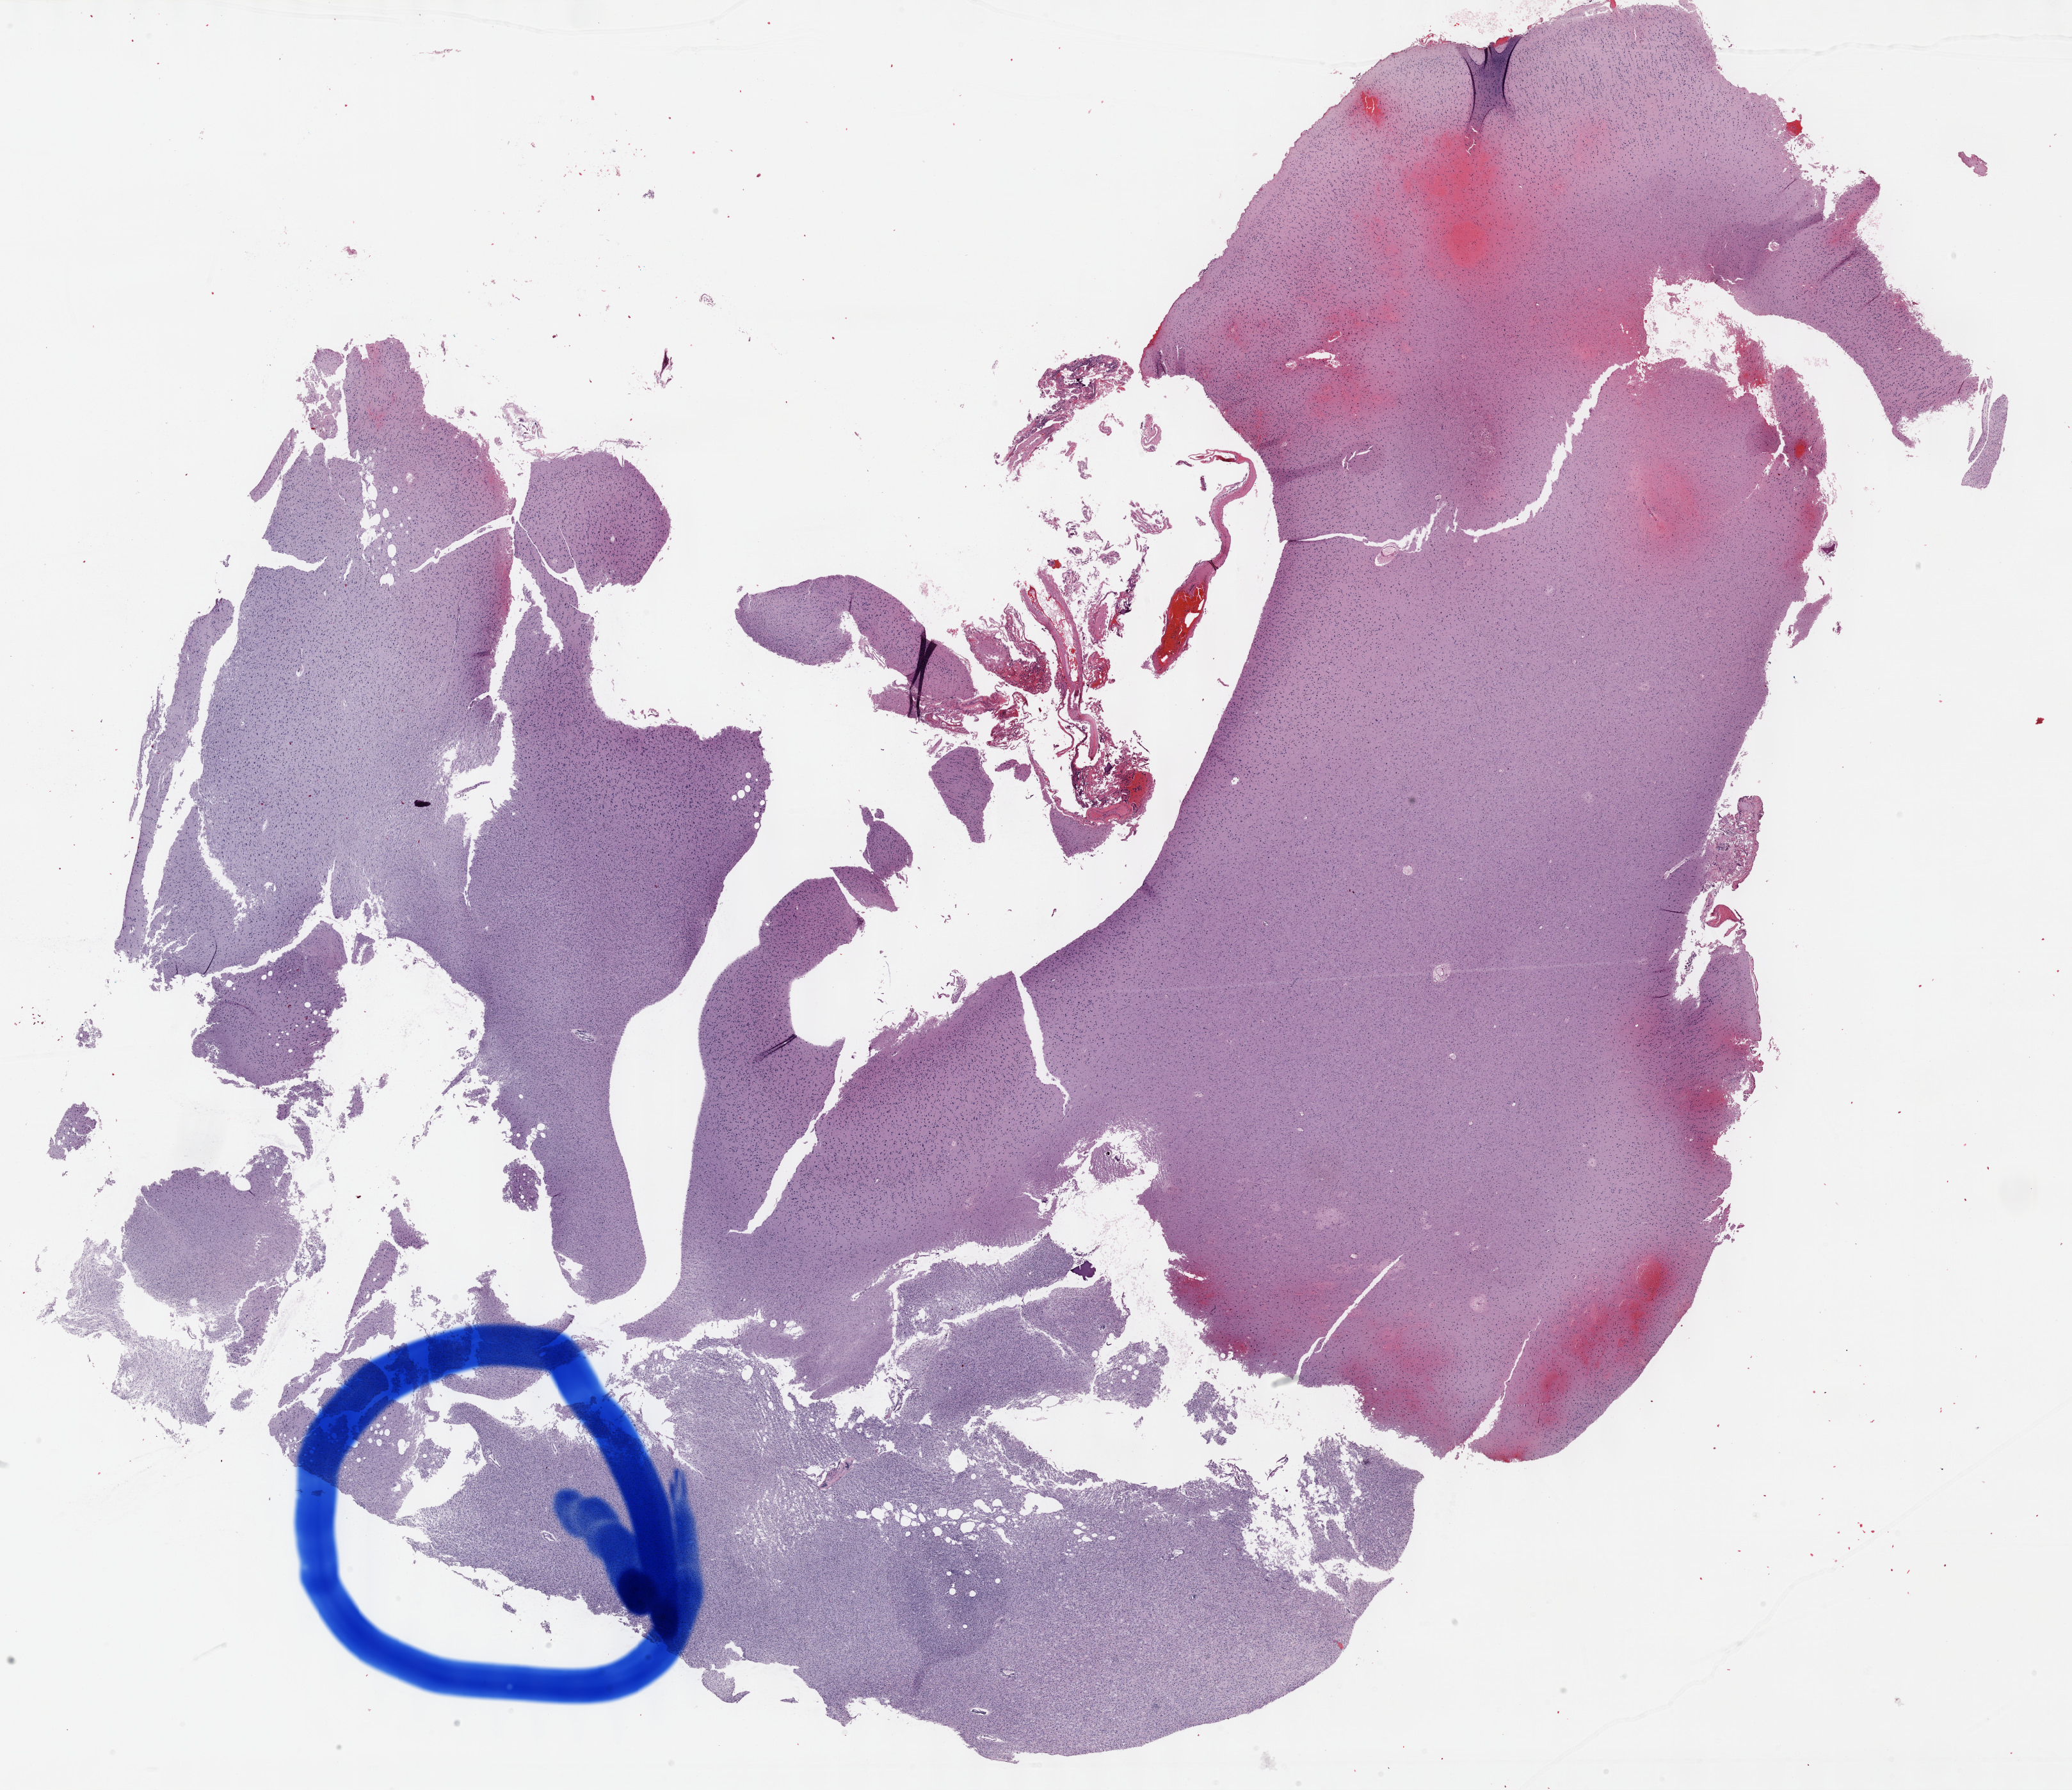
Digitized H&E-stained tissue section (whole slide), low-resolution overview of the scanned area, about 26.2 x 22.6 mm (slide scanned at 40x). Formalin-fixed paraffin-embedded (FFPE) diagnostic section. Brain, primary tumour sample. Patient: male, age at initial diagnosis 26 years. Histologic grade: G3 (poorly differentiated).
Pathologic diagnosis: Mixed glioma (cerebrum).